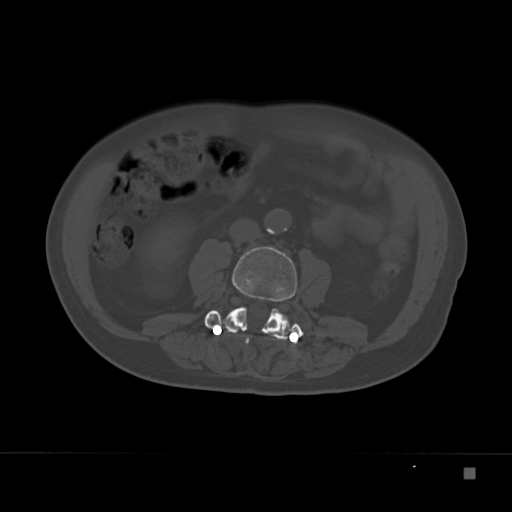
CT including the spine, one axial slice. Slice 62 of 332 in the series (ordered by position). Reconstruction kernel Br40s. Bone window (W 1800 / L 400 HU). 1.5 mm slice thickness. 512 × 512 image matrix, field of view 389 × 389 mm. Male patient, age 72 years. From the clinical record (not read from this slice): primary cancer: skeletal.
Annotated regions visible in this slice (semi-automatically segmented with operator editing):
- L3 vertebra: box from (x=204, y=246) to (x=304, y=339) px
- L4 vertebra: (x=268, y=324)–(x=298, y=342)